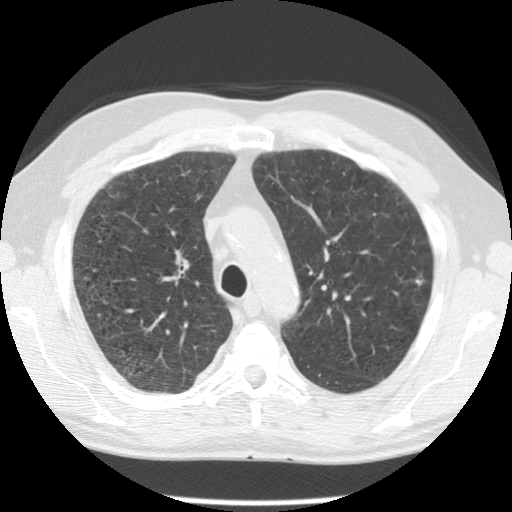
Axial slice from a low-dose chest CT screening exam, baseline screening round, lung window (W 1500 / L -600 HU), 120 kVp, slice 31 of 113 in the series. Male, age 59 years at enrolment. Current smoker at enrolment.
• Expert-annotated lung lesion, bounding box <402,262,443,302> (left, top, right, bottom; pixels).
• The screening reader recorded 2 non-calcified nodules or masses ≥4 mm on this exam; which of them this box marks is not recorded.
• Lung cancer was diagnosed 436 days after this screen: squamous cell carcinoma, NOS, left upper lobe, poorly differentiated (G3), stage IA (AJCC 6th edition), 10 mm at pathology.